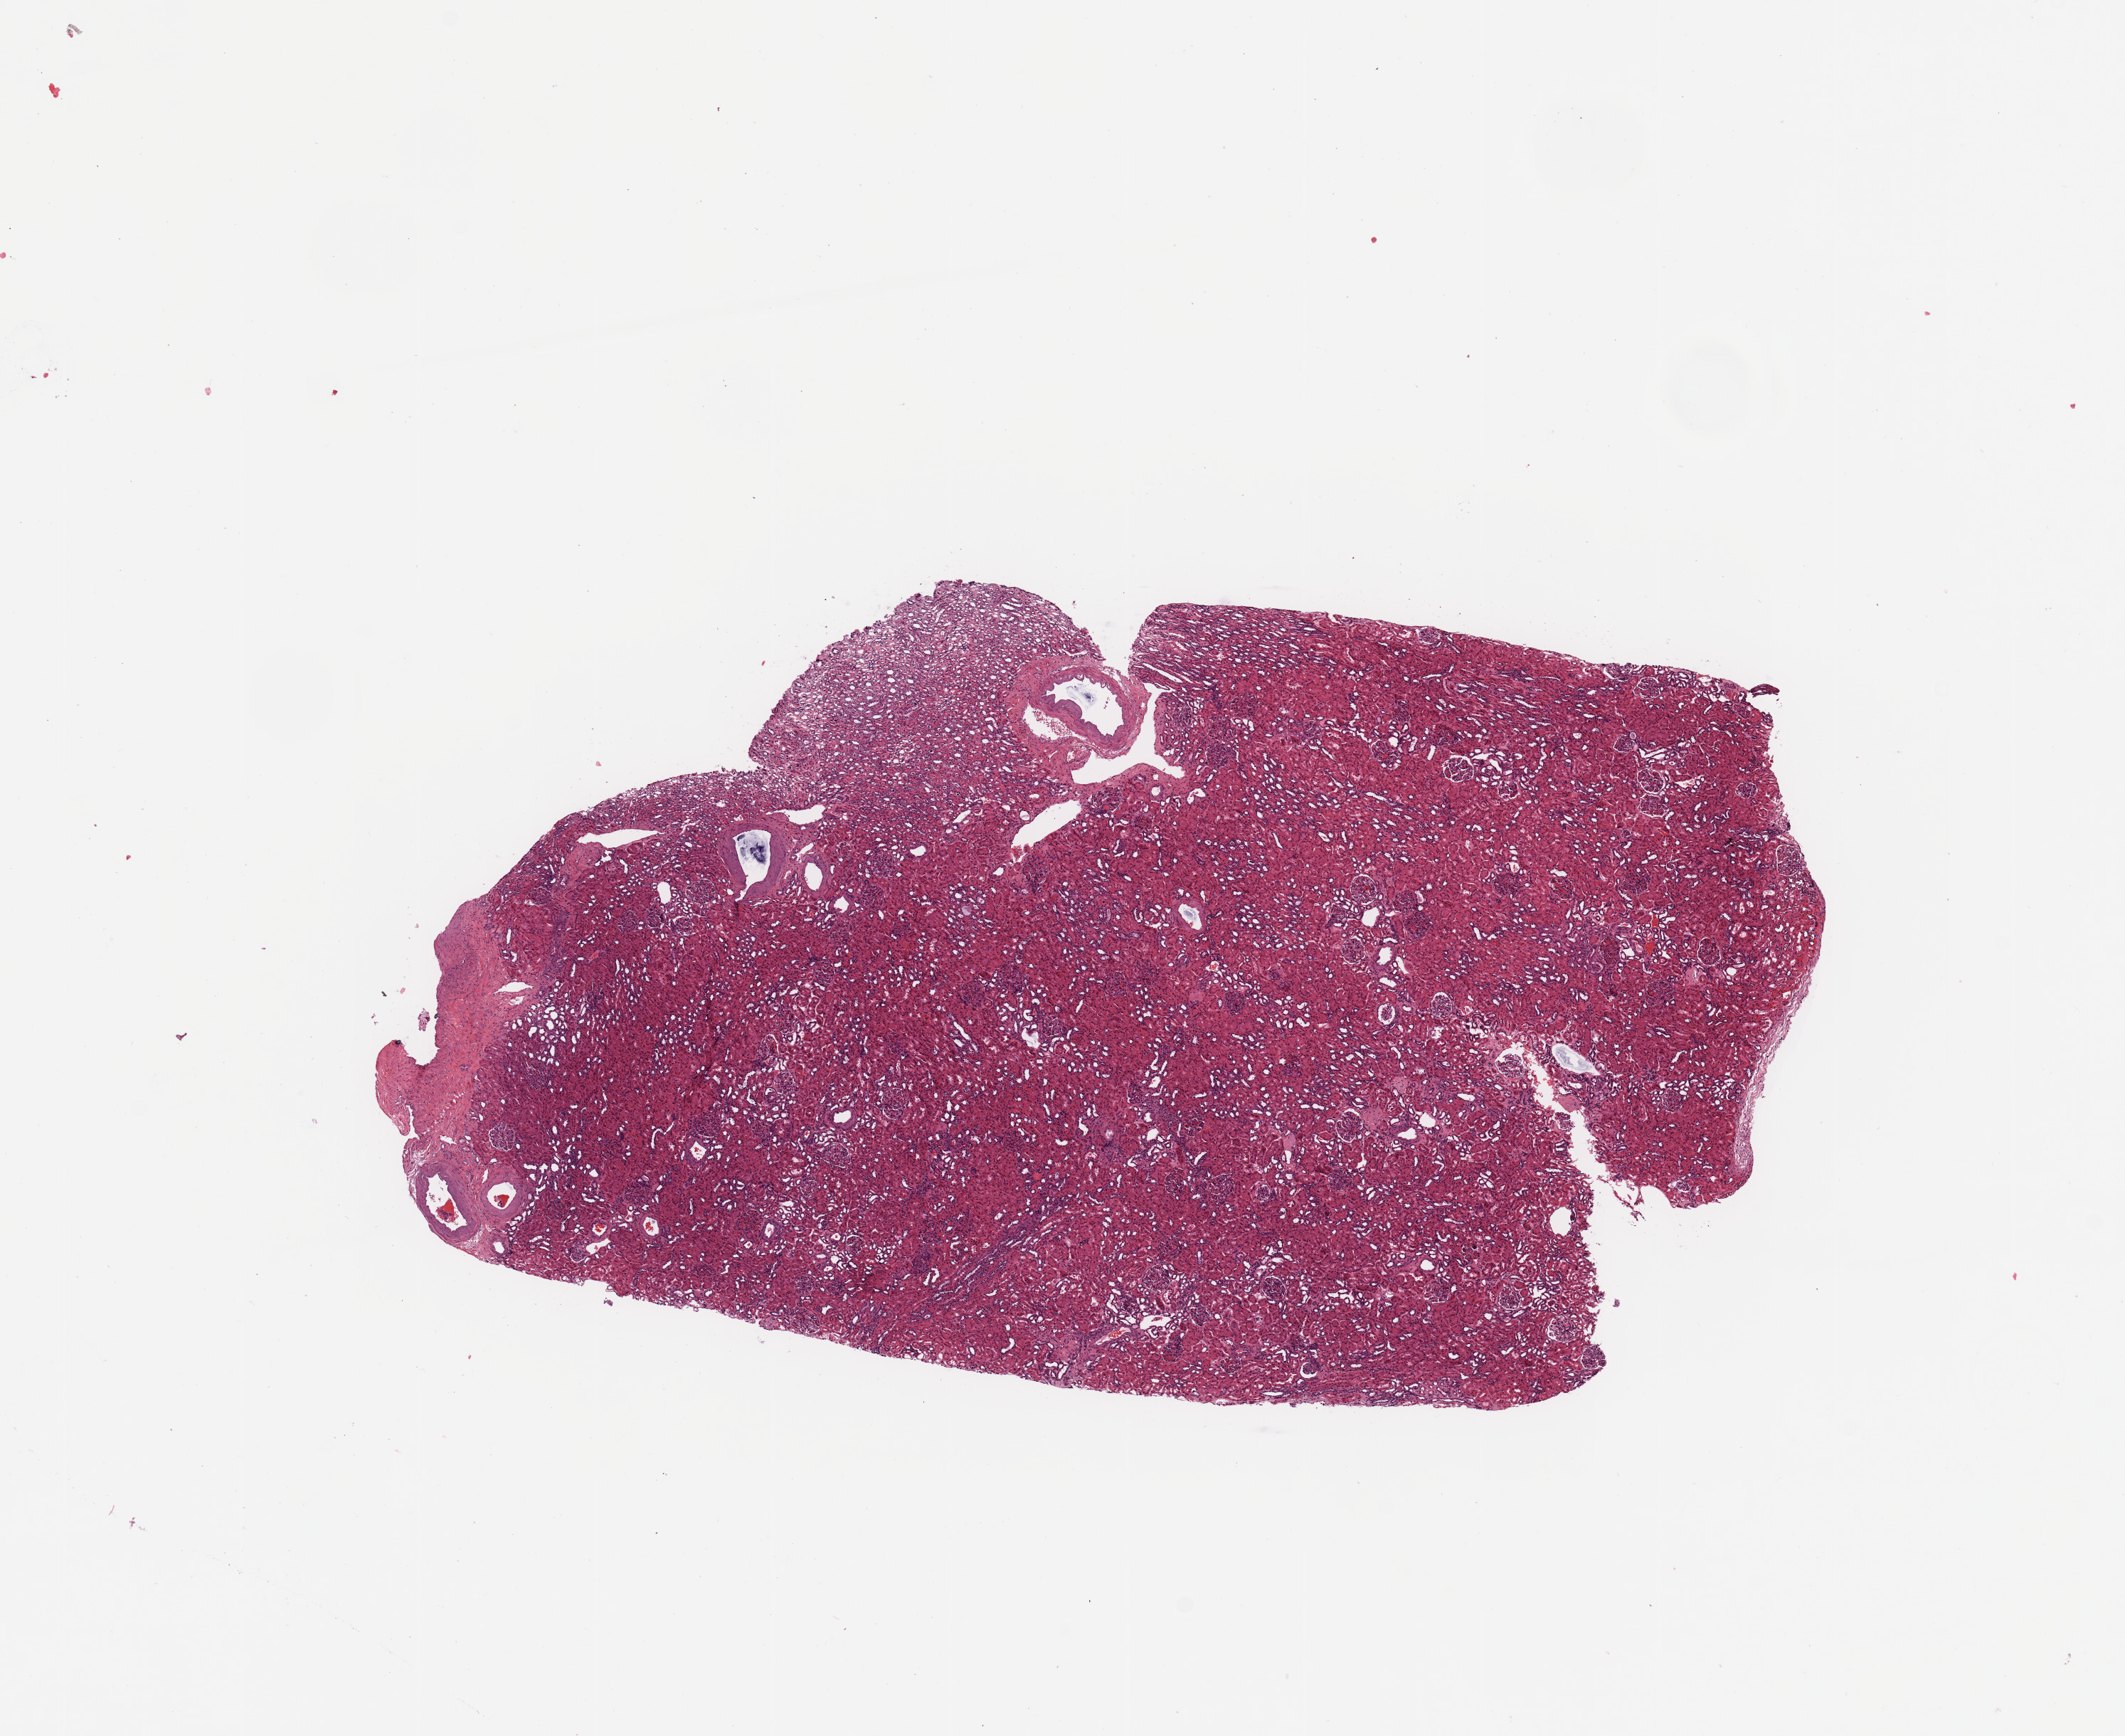
H&E whole-slide image — low-resolution overview of the scanned area, about 11.8 x 9.6 mm (acquisition: 20x scan); normal (non-tumour) tissue sample, sampled site: kidney. Female, 57 y/o.
• this section: normal (non-tumour) tissue from the same patient
• patient diagnosis: Renal cell carcinoma, NOS